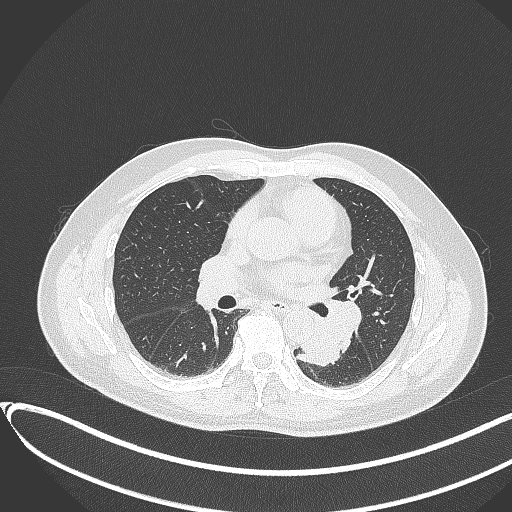
Chest CT, one axial slice. Position 182 of 417 along the scan axis. Lung window (W 1500 / L -600 HU). 1 mm slice thickness. 512 × 512 image matrix, field of view 400 × 400 mm. Male patient, age 54 years. From the clinical record (not read from this slice): clinical TNM (as recorded): T3 N0 M0.
Annotated regions visible in this slice (rectangle marked by the reading radiologist):
- lung tumour (recorded histology: squamous cell carcinoma): box from (x=294, y=317) to (x=341, y=367) px